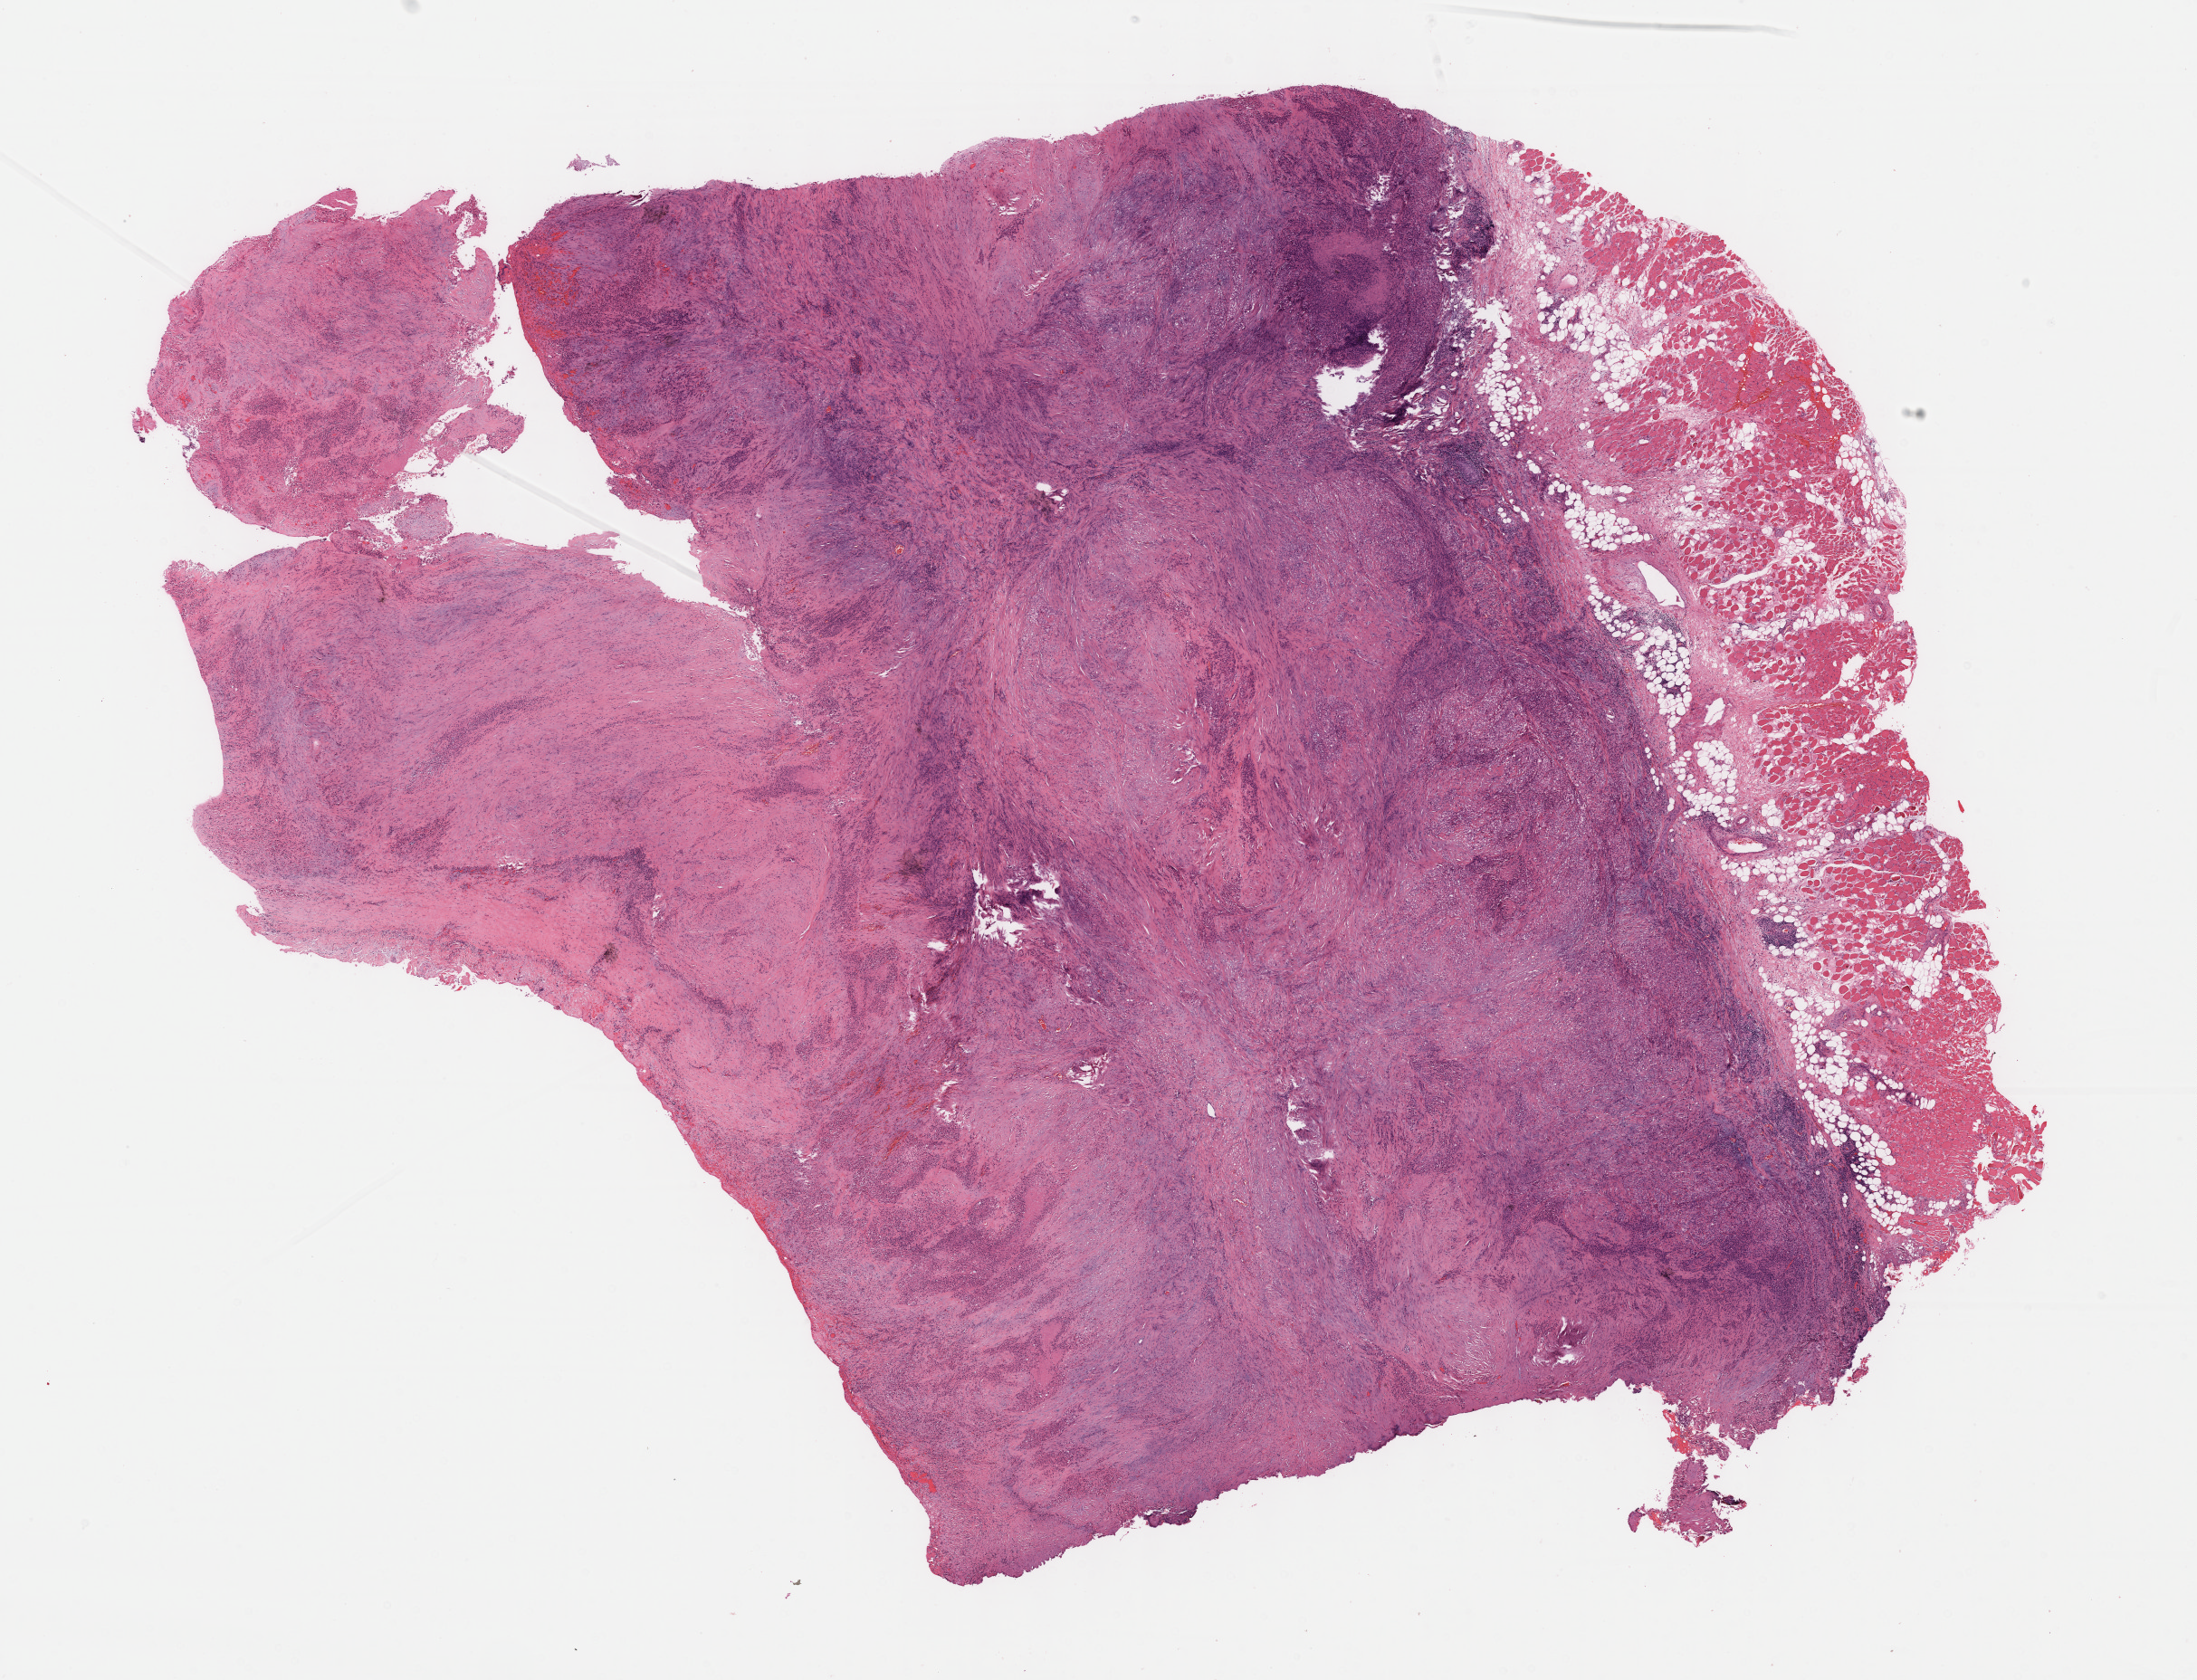
Whole-slide histology image, Hematoxylin and eosin (H&E) stained, low-resolution overview of the scanned area, about 19.6 x 15.0 mm, formalin-fixed paraffin-embedded (FFPE) diagnostic section, sample: primary tumour, mesothelium. Male, age 52 years at initial diagnosis.
AJCC pathologic stage: I (6th edition). Histologic diagnosis: Epithelioid mesothelioma, malignant. Laterality: right.